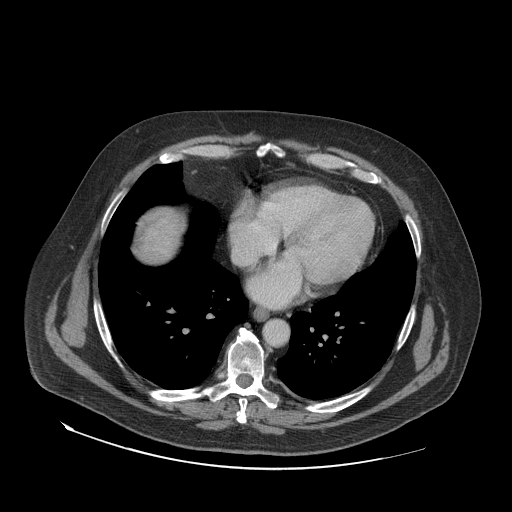
Contrast-enhanced abdominal CT (liver protocol), one axial slice. Reconstruction kernel STANDARD. Soft-tissue window (W 400 / L 40 HU). 2.5 mm slice thickness. 512 × 512 image matrix, field of view 480 × 480 mm. From the clinical record (not read from this slice): diagnosis: hepatocellular carcinoma (patient treated with transarterial chemoembolisation; whether this scan precedes or follows treatment is not stated here); TNM stage (as recorded): Stage-IVA.
Annotated regions visible in this slice (semi-automatically segmented with operator editing):
- liver parenchyma outside the tumour (the mass and vessels are separate outlines, so this box may not span the whole liver): bounding box (x1, y1, x2, y2) in pixels: (140, 210, 183, 262)
- mass: (144, 214, 179, 256)